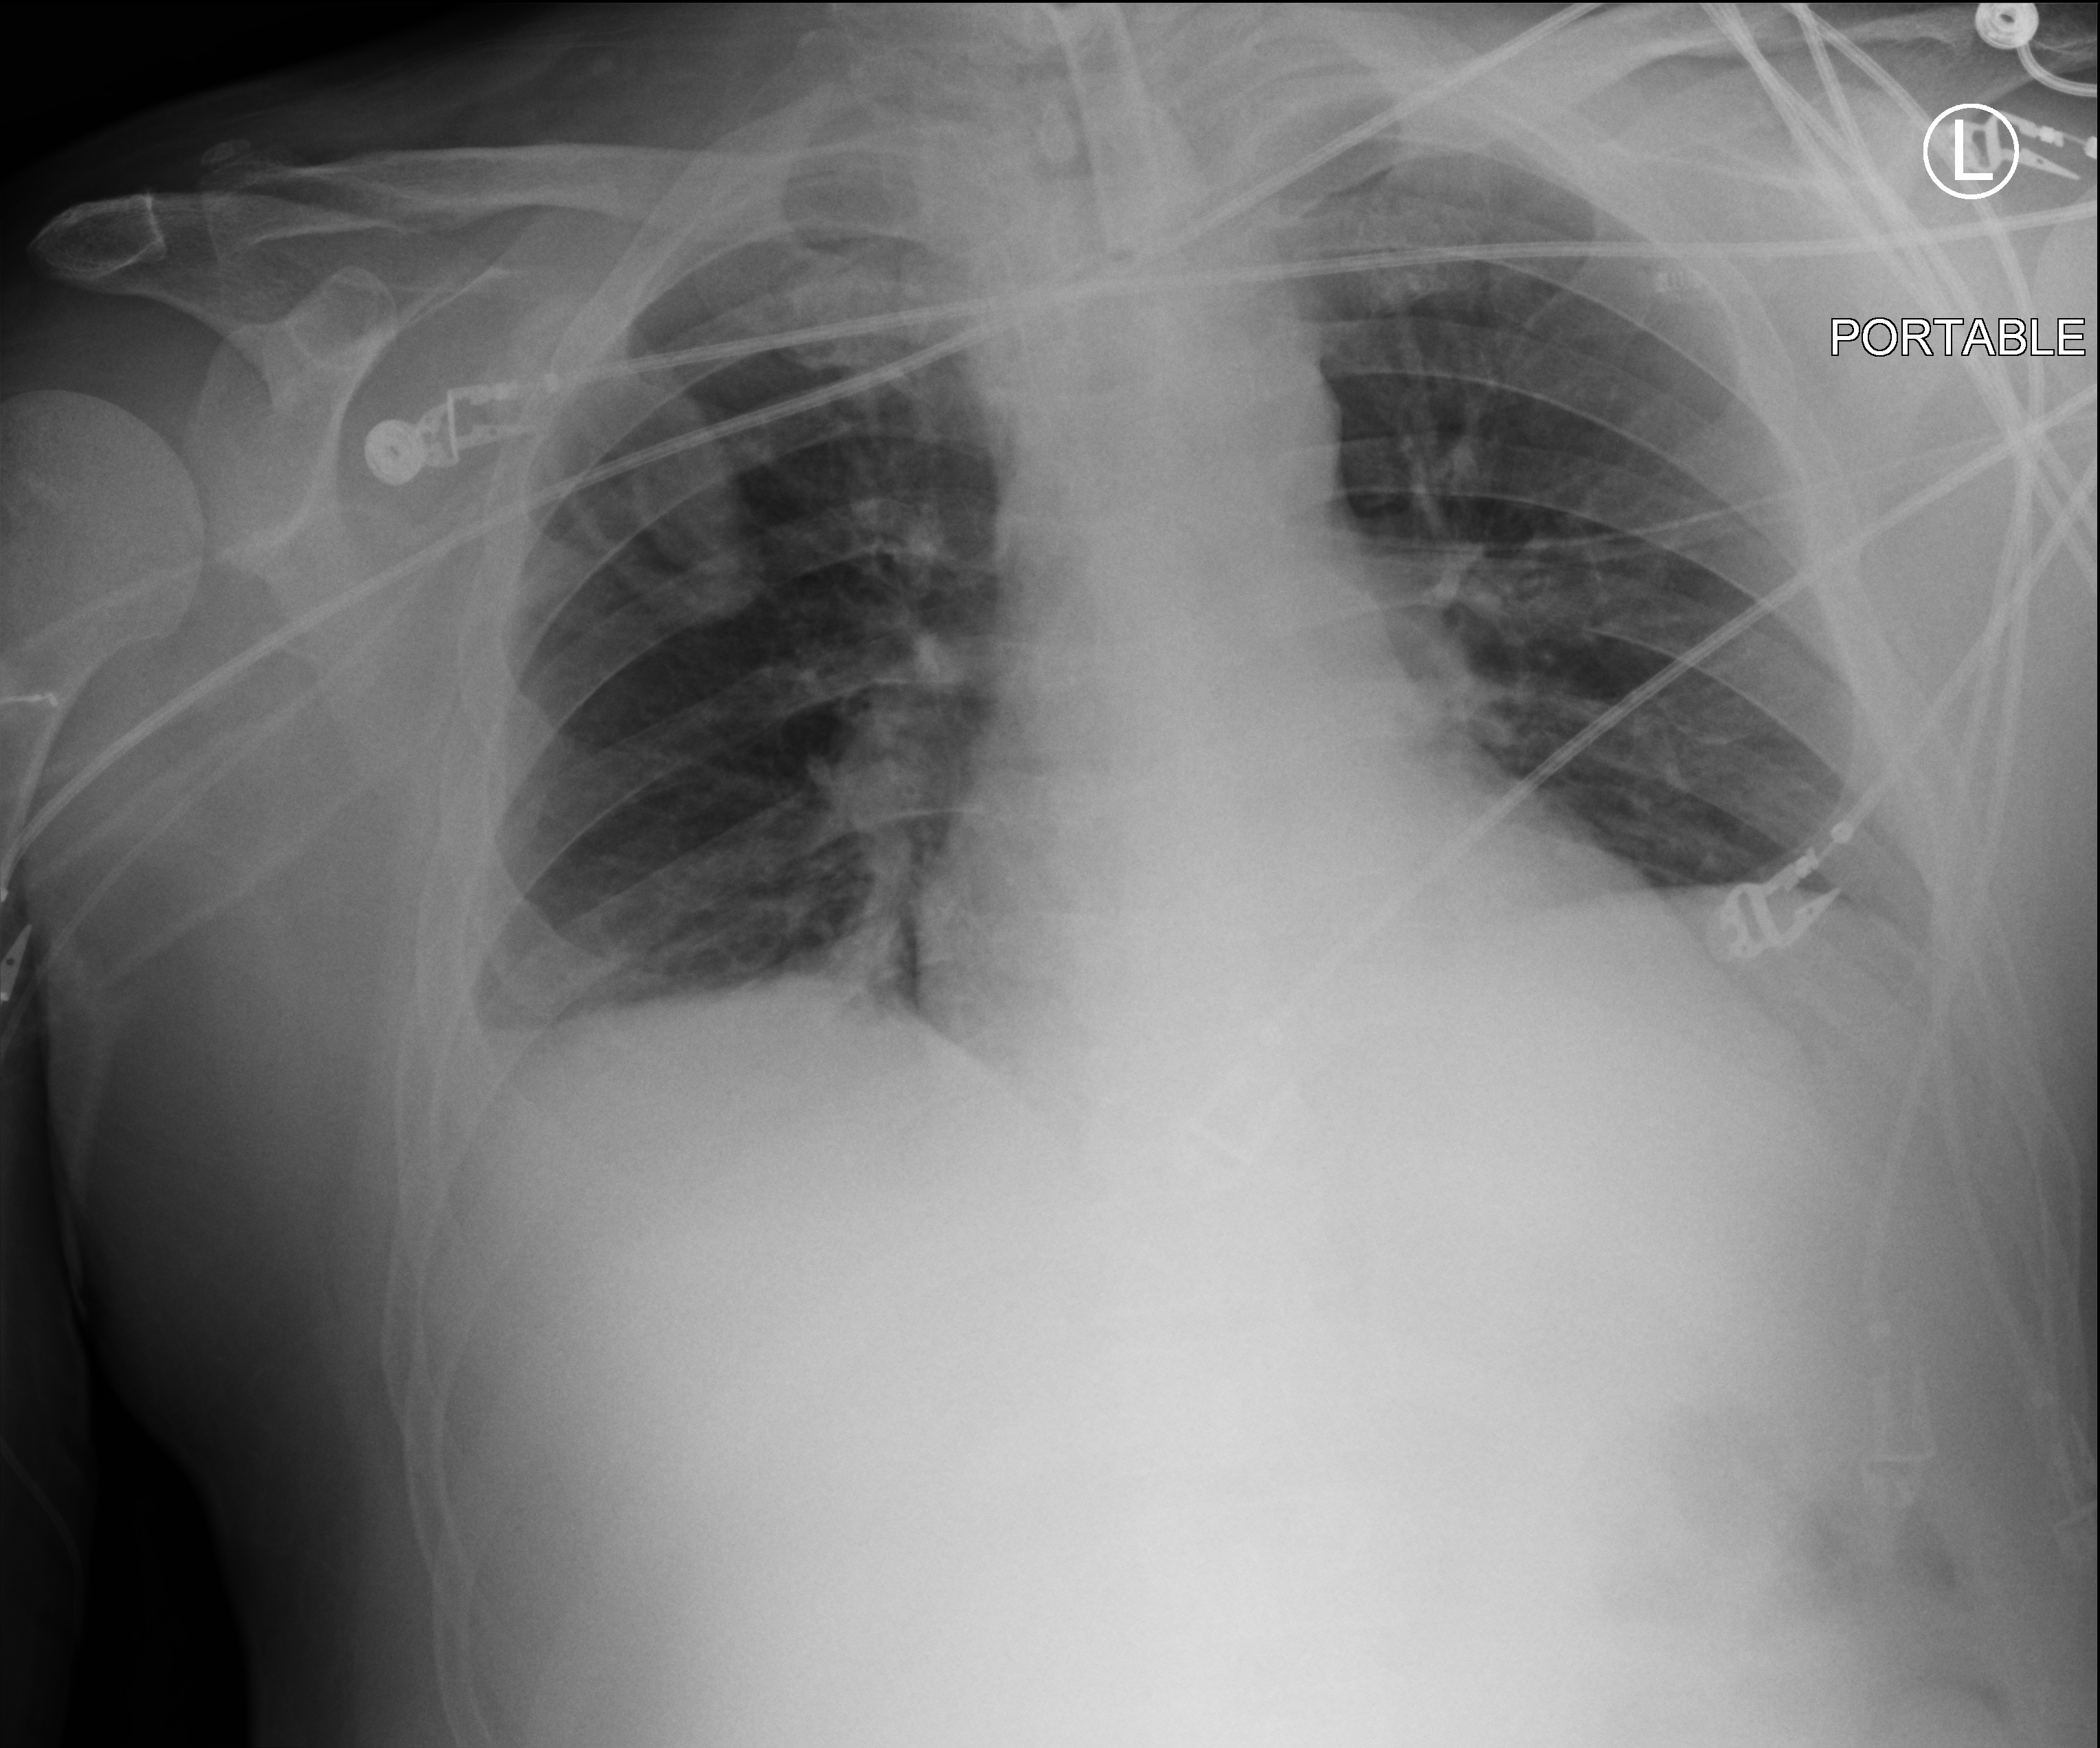
Portable chest radiograph; anteroposterior (AP) projection. Patient hospitalised with COVID-19; male, aged 18–59 years.
Hospital-stay facts (about this admission, not read from this image; timing relative to this image not recorded):
- admitted to intensive care during this hospital stay: yes